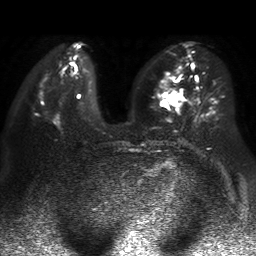
Breast MRI, one axial slice. Position 19 of 50 along the scan axis. Diffusion-weighted series; image 2 of 4 stored at this slice position (different b-values; order by instance number). 1.5 T. 256 × 256 image matrix. Female patient.
Structures marked on this image (manually delineated by an expert):
- tumour on diffusion-weighted imaging: bounding box [x1, y1, x2, y2] px = [169, 94, 181, 104]